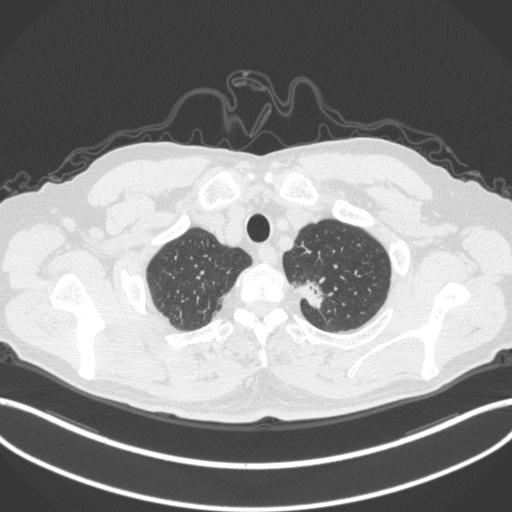
Chest CT, one axial slice; position 340 of 382 along the scan axis; reconstruction kernel B31f; 120 kVp; lung window (W 1500 / L -600 HU); 512 × 512 image matrix, field of view 400 × 400 mm. Patient: male, 64 years. From the clinical record (not read from this slice): clinical TNM (as recorded): T1c N0 M0.
Outlined on this slice (rectangle marked by the reading radiologist):
- lung tumour (recorded histology: adenocarcinoma): box from (x=296, y=272) to (x=330, y=313) px